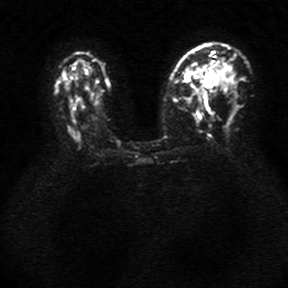
Breast MRI, one axial slice. Diffusion-weighted series; image 2 of 4 stored at this slice position (different b-values; order by instance number). 1.5 T. 288 × 288 image matrix, field of view 340 × 340 mm. Female patient.
Outlined on this slice (outlined manually by an expert reader):
- tumour on diffusion-weighted imaging: bounding box [x1, y1, x2, y2] px = [204, 72, 218, 87]